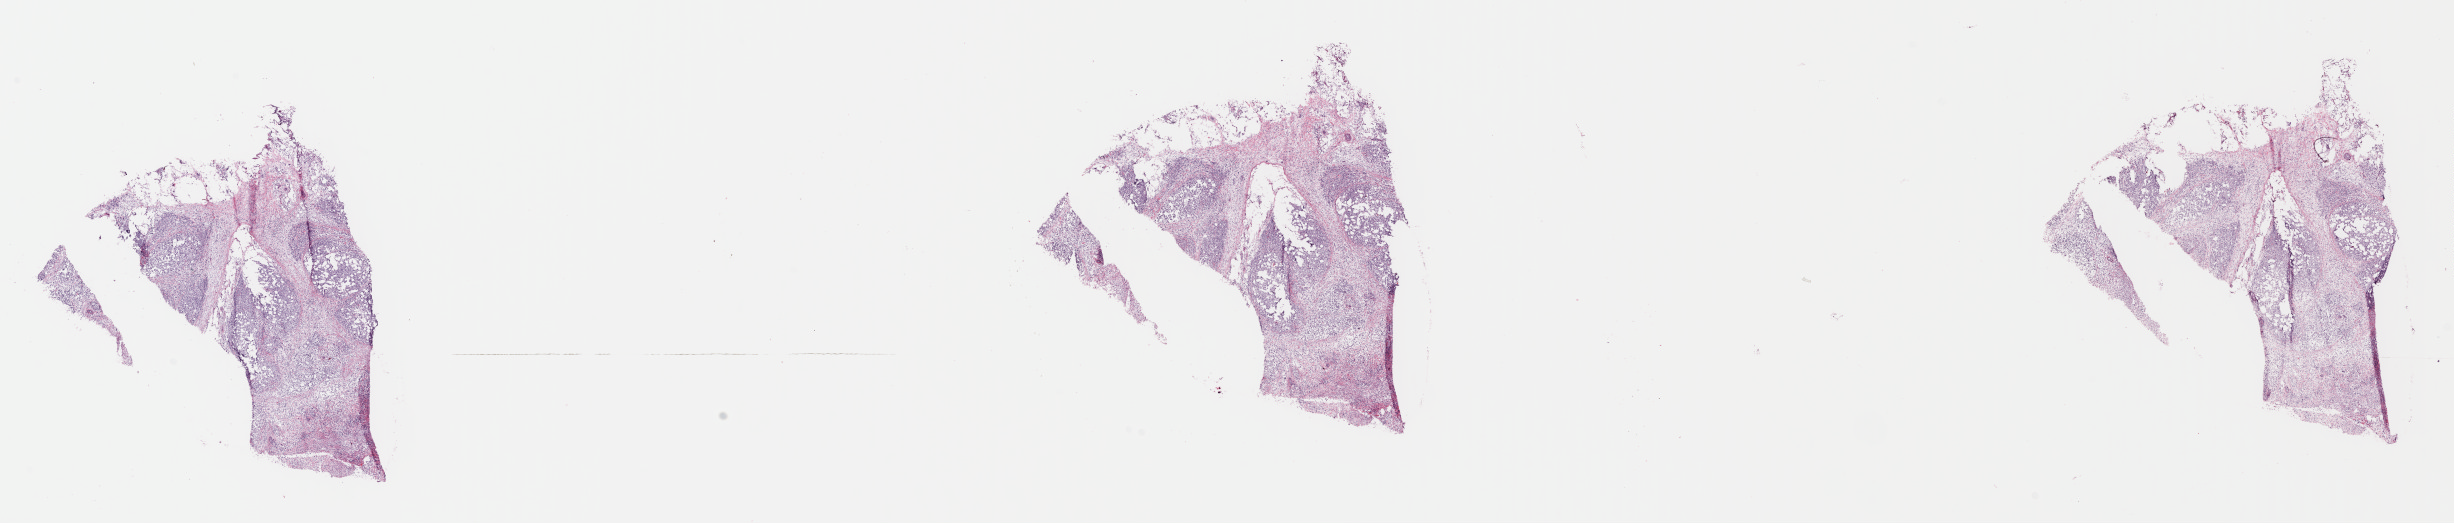
Whole-slide histology image, H&E-stained — shown as a low-resolution overview of the whole scanned area (about 38.6 x 8.2 mm, from a 40x scan), frozen section from the top of the tissue portion, sample: primary tumour, stomach. Female, age 41 years at initial diagnosis. Histologic grade: G3 (poorly differentiated). Pathologist review of this section (percent, as recorded): tumour cells 60%, tumour nuclei 80%, normal cells 10%, stromal cells 30%, necrosis 0%. Infiltration values recorded for this section: lymphocyte infiltration 0%, monocyte infiltration 0%, neutrophil infiltration 0%.
- diagnosis: Carcinoma, diffuse type (fundus of stomach)
- TNM: T4a N3 M1
- lymph nodes positive (case pathology): 12 of 16 examined
- AJCC pathologic stage: IV (7th edition)